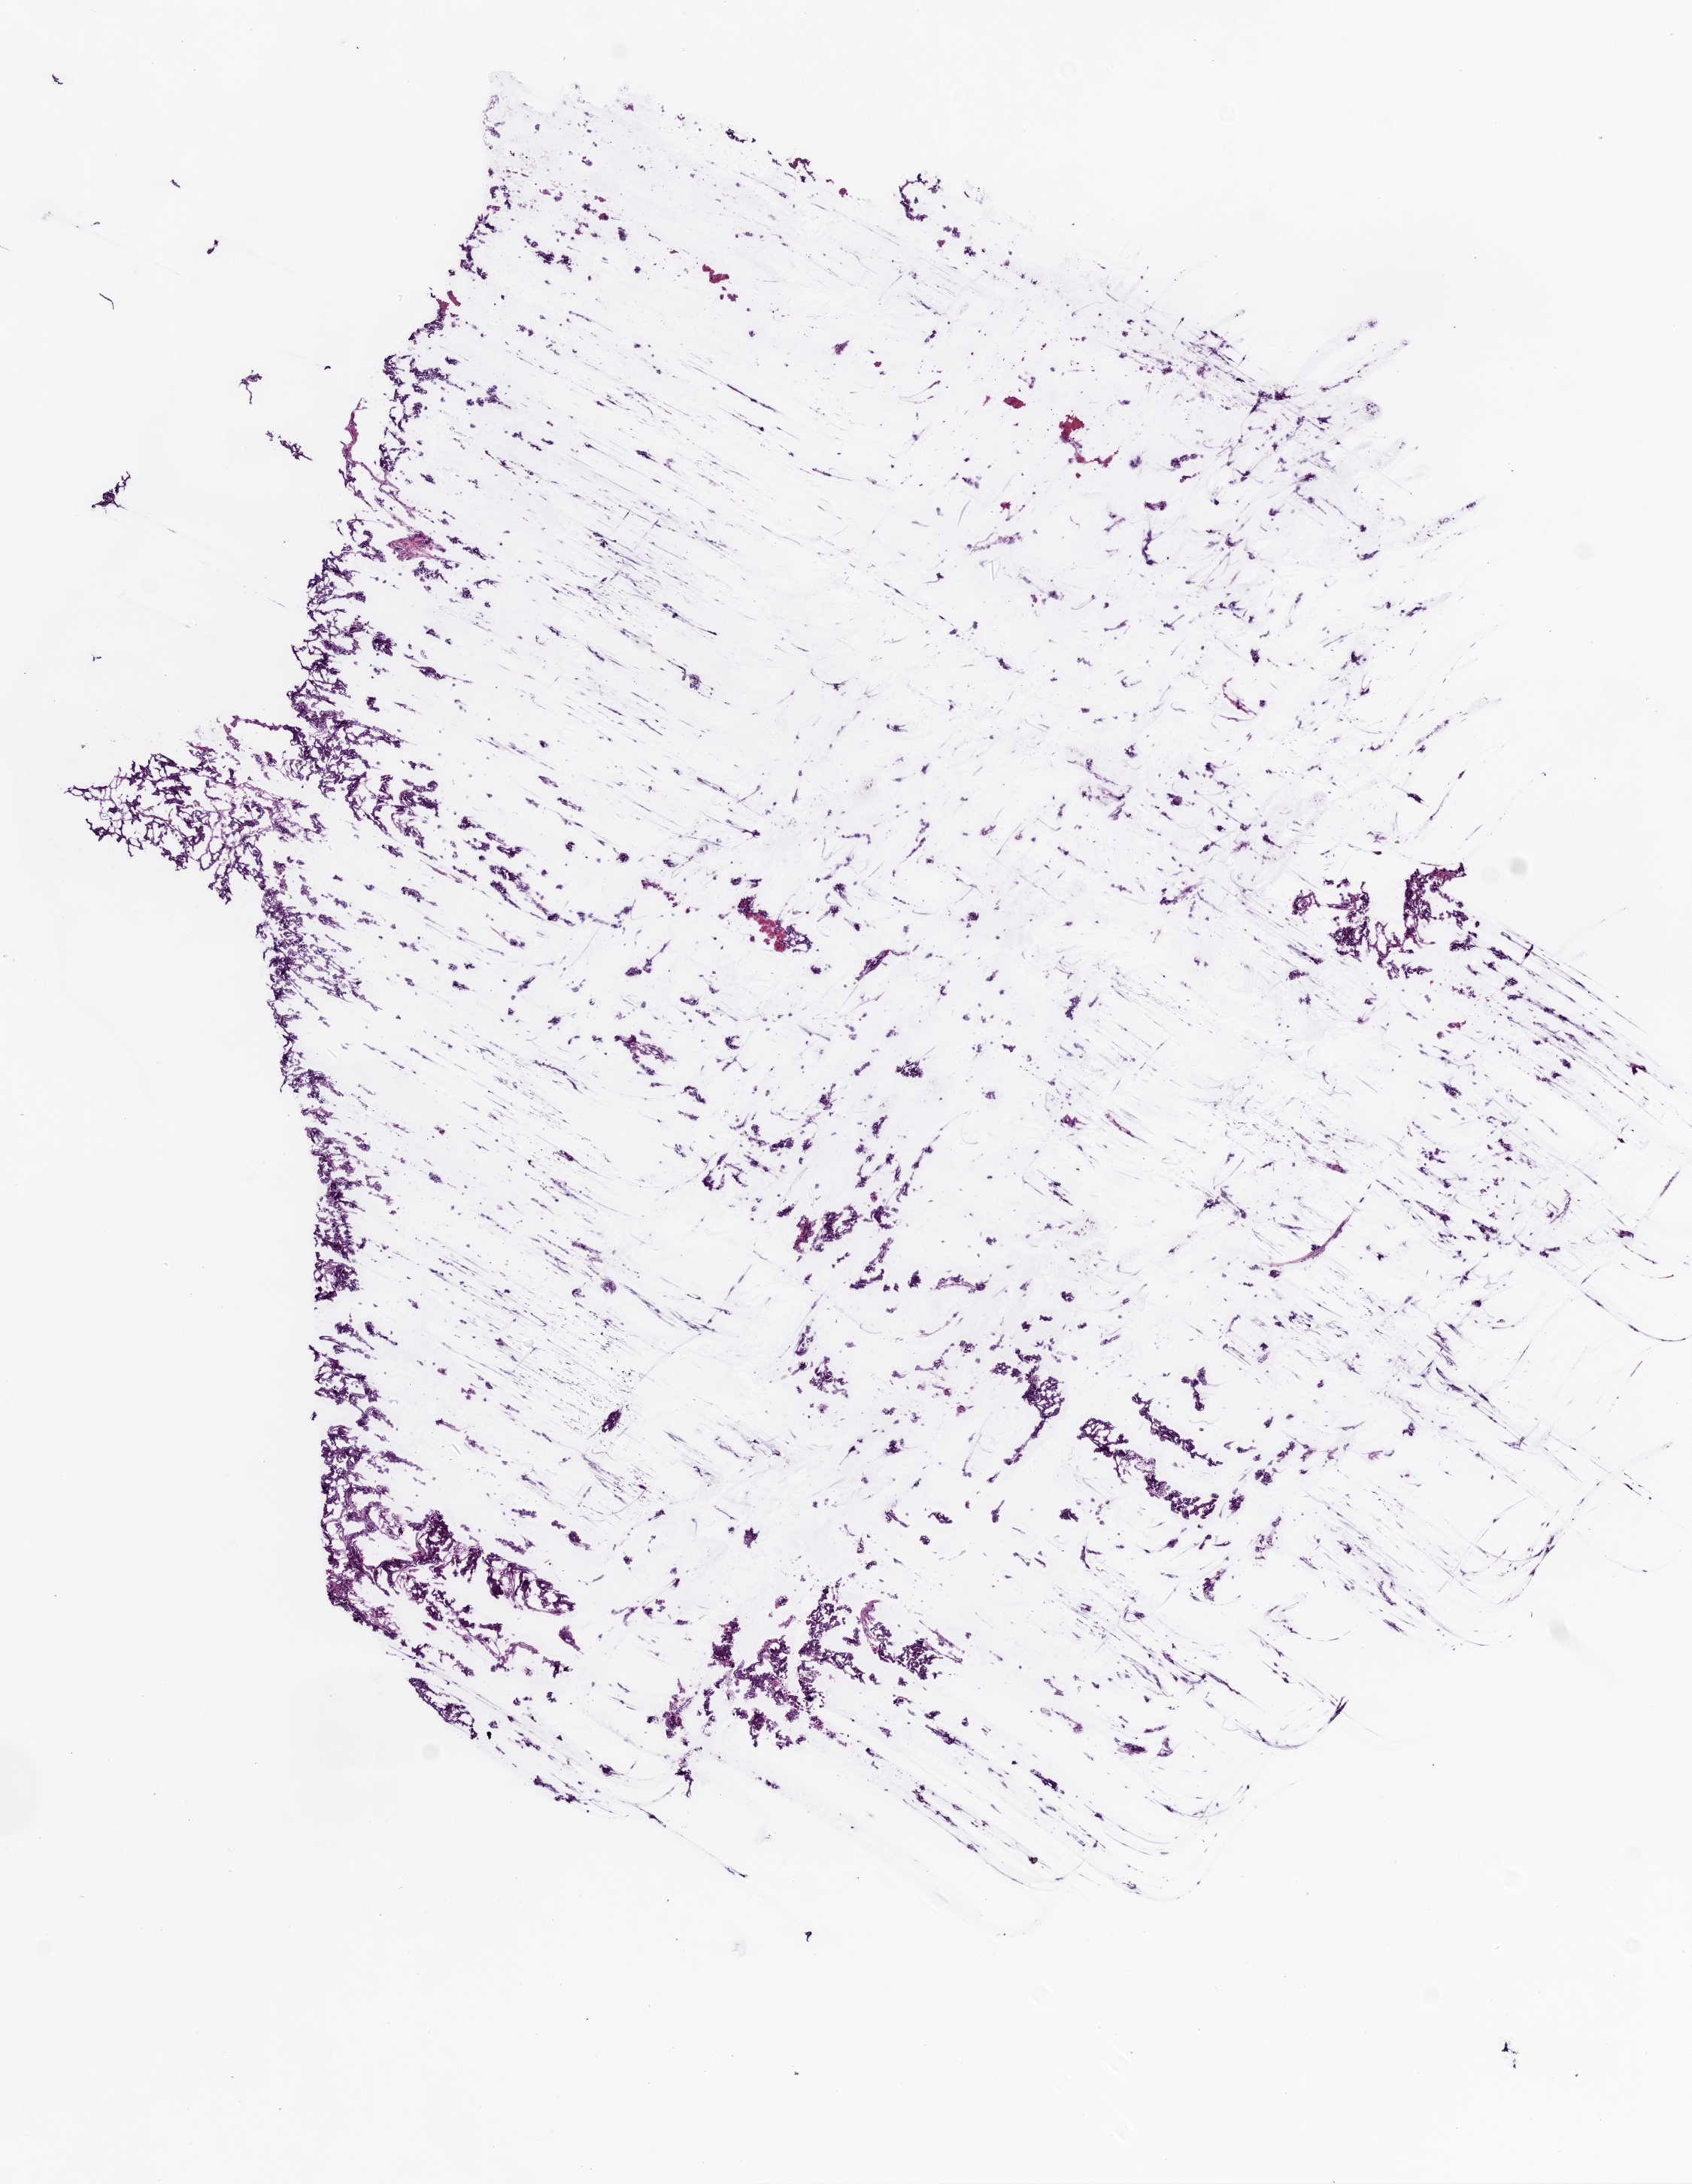
Digitized H&E-stained tissue section (whole slide) — low-resolution overview of the scanned area, about 9.0 x 11.7 mm; frozen section from the top of the tissue portion; ovary, primary tumour sample. Female, age 69 years at initial diagnosis. Histologic grade: G3 (poorly differentiated). Composition of this section per pathologist review: tumour cells 90%, tumour nuclei 73%, normal cells 5%, stromal cells 0%, necrosis 5%.
* pathologic diagnosis: Serous cystadenocarcinoma, NOS
* FIGO stage: IIIC